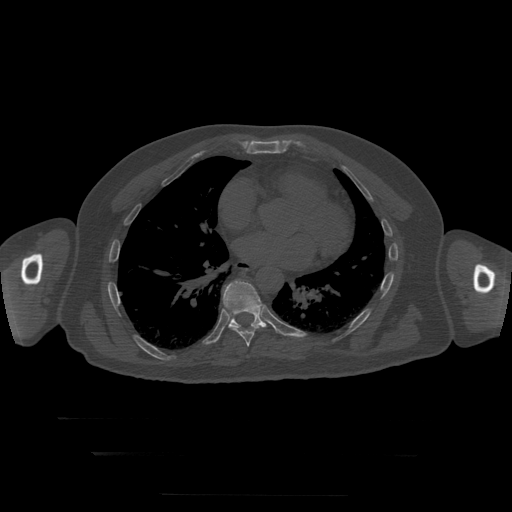
CT including the spine, one axial slice. Reconstruction kernel STANDARD. Bone window (W 1800 / L 400 HU). 512 × 512 image matrix, field of view 510 × 510 mm. Patient age 73 years. From the clinical record (not read from this slice): primary cancer: prostate.
Structures marked on this image (semi-automatically segmented with operator editing):
- T8 vertebra: bounding box <226,302,260,347> (left, top, right, bottom; pixels)
- T9 vertebra: <223,281,267,328>